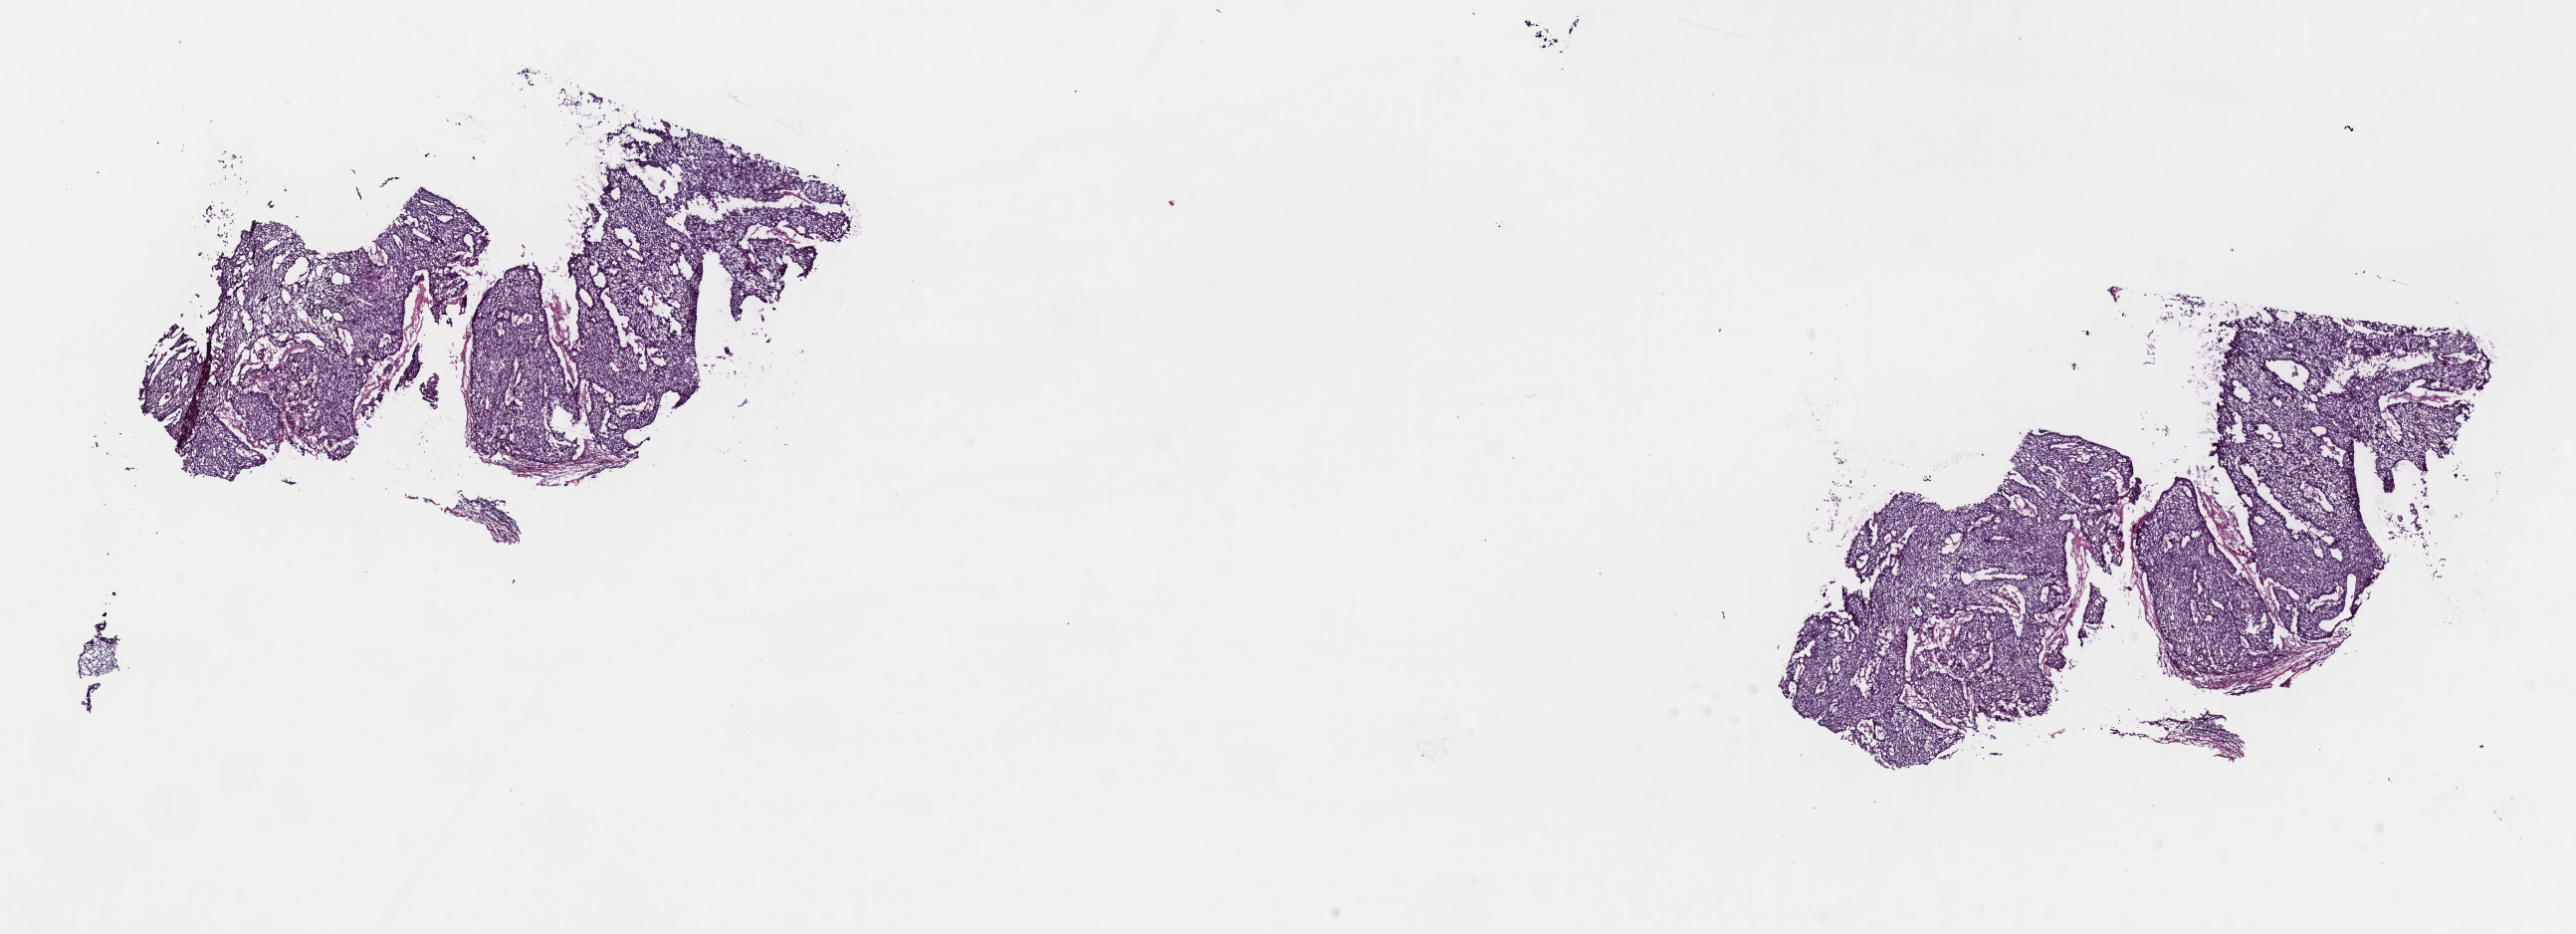
Whole-slide histology image, H&E — shown as a low-resolution overview of the whole scanned area (about 20.4 x 7.4 mm). Frozen section. Sample: primary tumour, esophagus. Male patient; age at initial diagnosis 77 years. Histologic grade: G2 (moderately differentiated). Pathologist review of this section (percent, as recorded): tumour cells 85%, tumour nuclei 85%, normal cells 0%, stromal cells 14%, necrosis 1%. Infiltration values recorded for this section: lymphocyte infiltration 2%, monocyte infiltration 1%, neutrophil infiltration 1%.
TNM: T3 N0 M0. AJCC pathologic stage: IIA (6th edition). Diagnosis: Squamous cell carcinoma, NOS (middle third of esophagus).